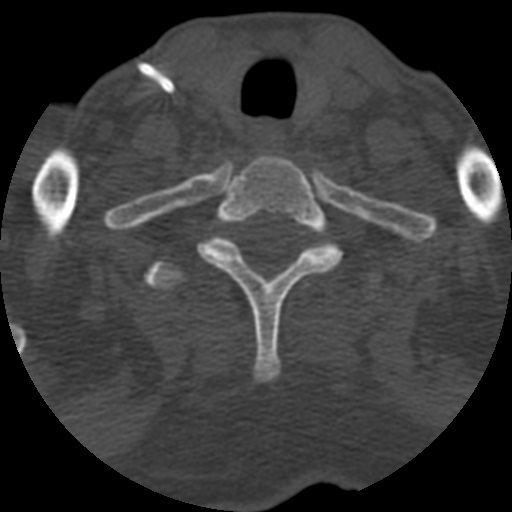
CT including the spine, one axial slice; position 516 of 708 along the scan axis; reconstruction kernel STANDARD; 120 kVp; one of 3 acquisitions stored at this slice position; bone window (W 1800 / L 400 HU); 1.25 mm slice thickness; 512 × 512 image matrix, field of view 160 × 160 mm. Patient age 55 years. Case-level facts recorded for this patient, not image findings: primary cancer: colon; vertebrae with lytic lesions (as recorded): T12, L1, L5.
Outlined on this slice (semi-automatic segmentation, software-assisted and operator-edited):
- T1 vertebra: bounding box <197,154,344,381> (left, top, right, bottom; pixels)
- T2 vertebra: <146,235,382,291>